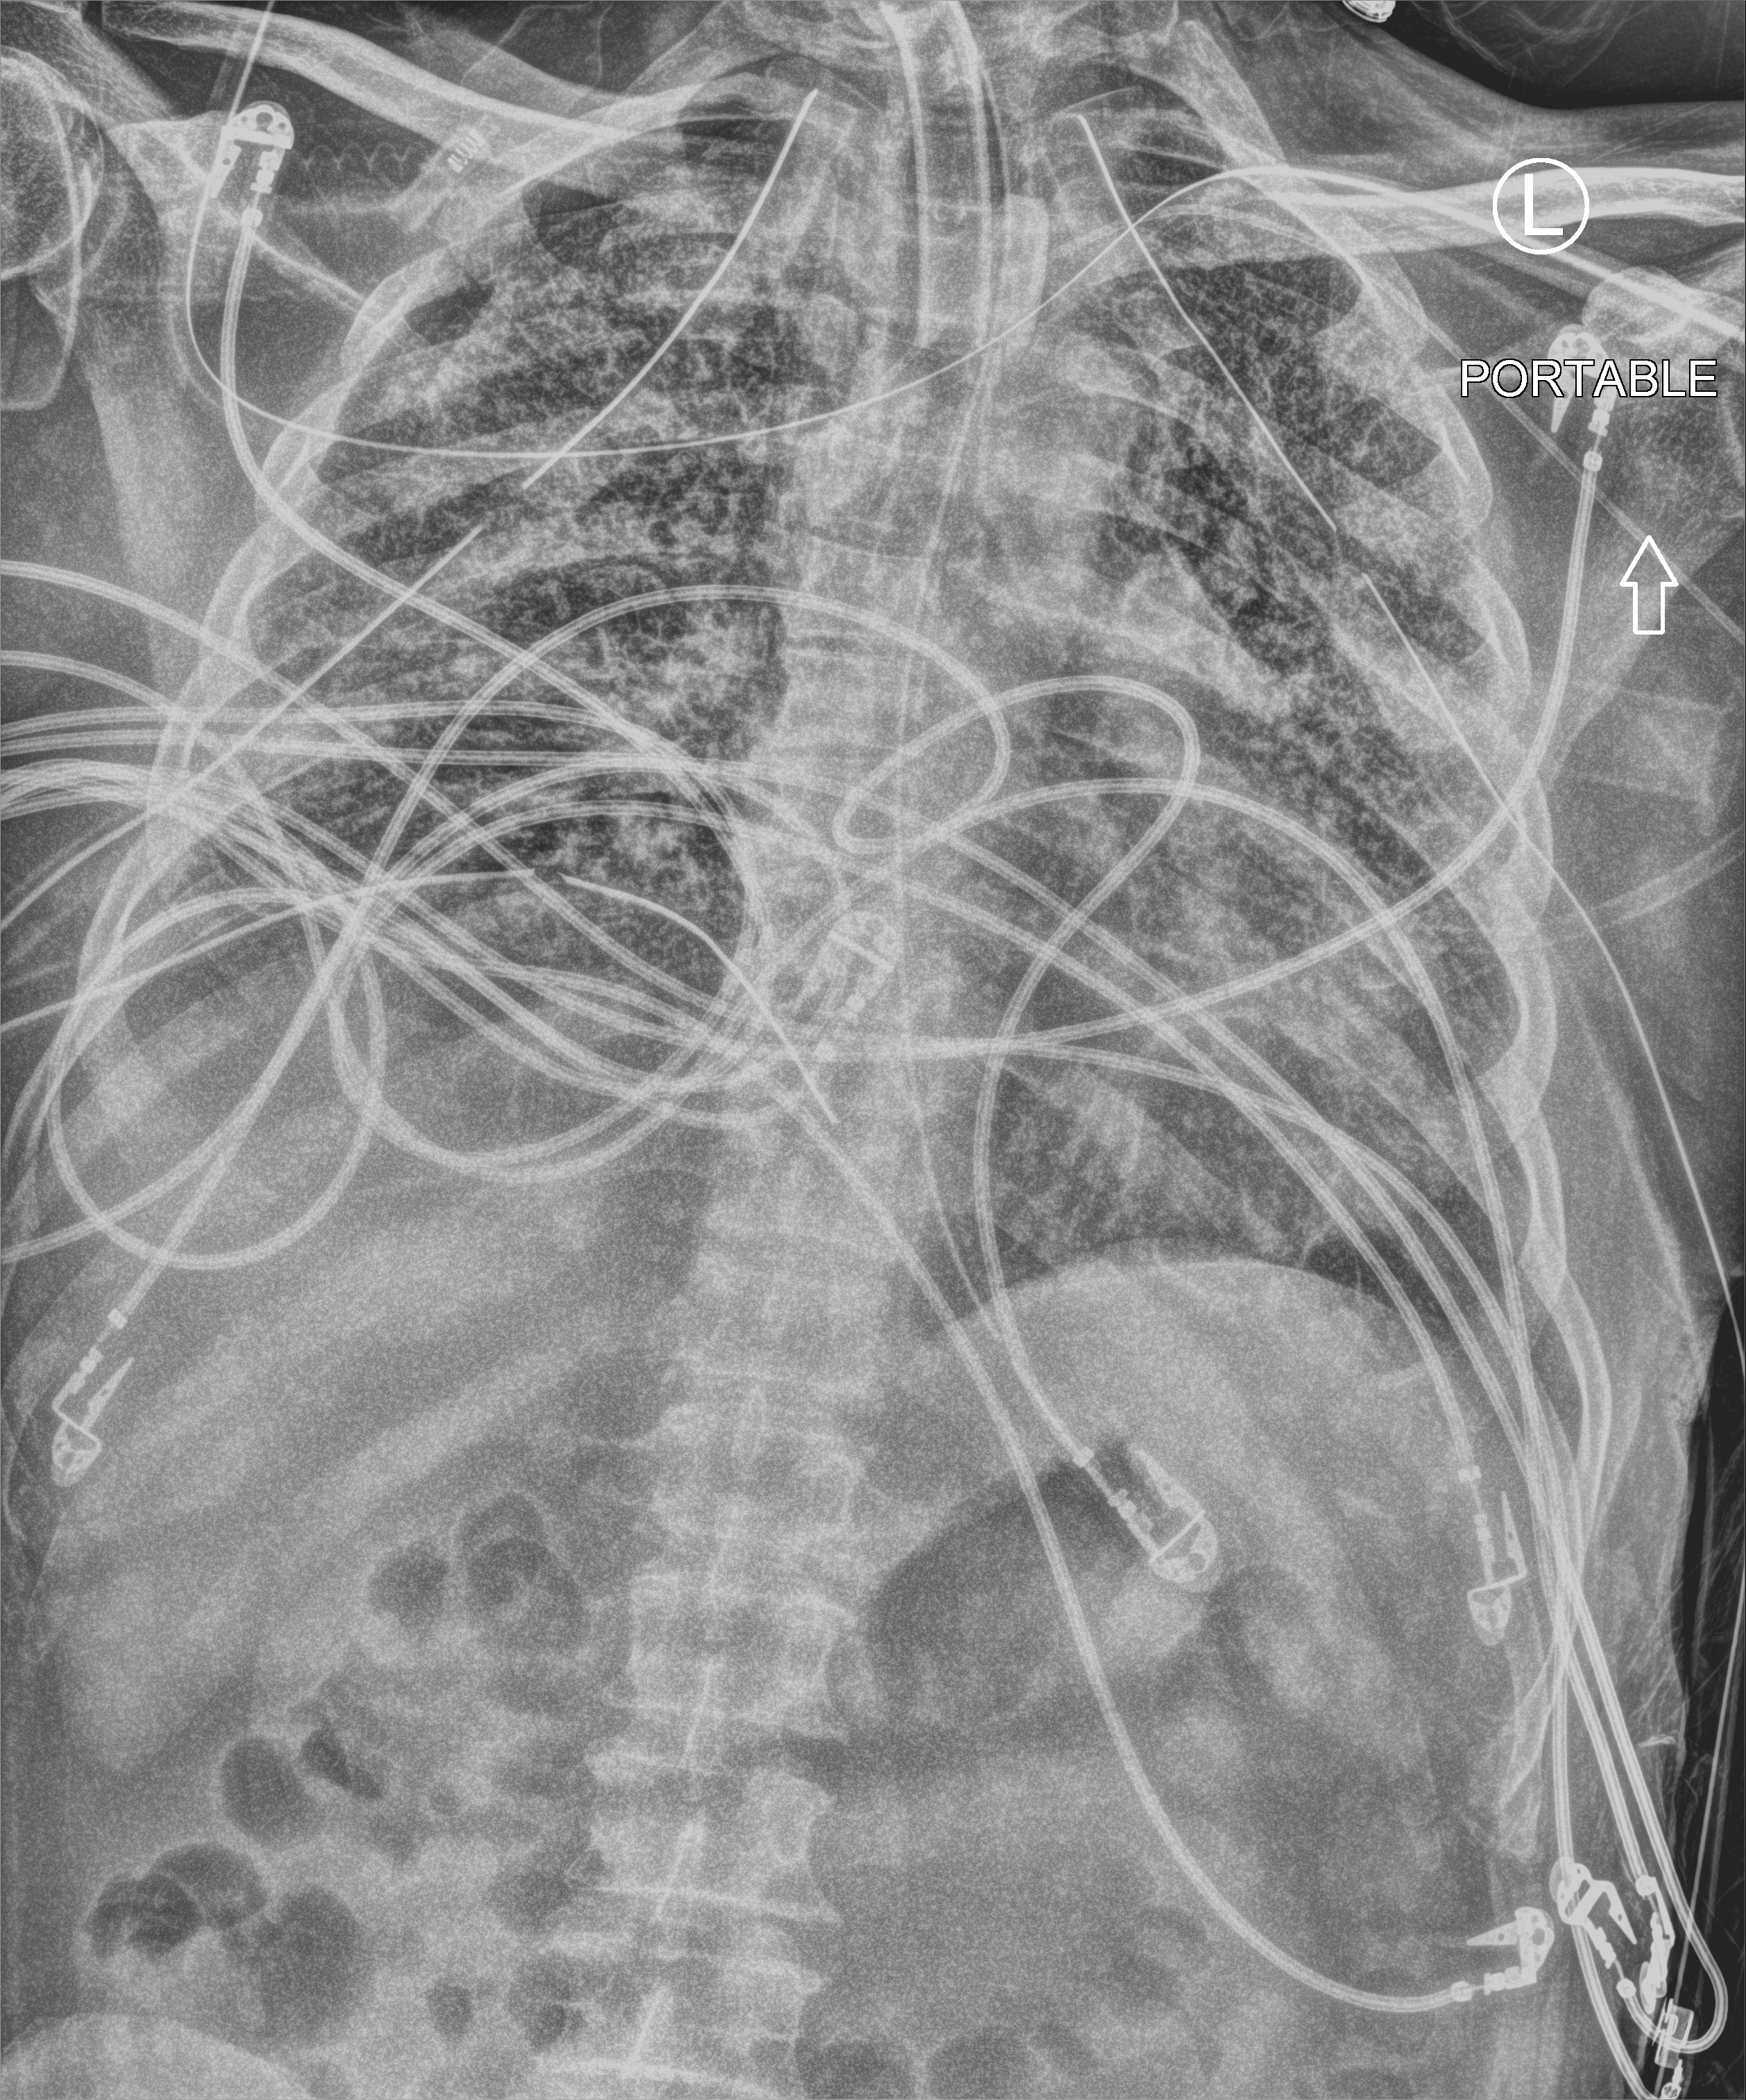
Bedside chest radiograph (computed radiography), anteroposterior (AP) projection. Male patient hospitalised with COVID-19, age 18–59 years.
Admission-level facts for this patient (not findings on this image; timing relative to this image not recorded): admitted to intensive care during this hospital stay: yes; mechanically ventilated during this hospital stay: yes; length of hospital stay: 83 days.